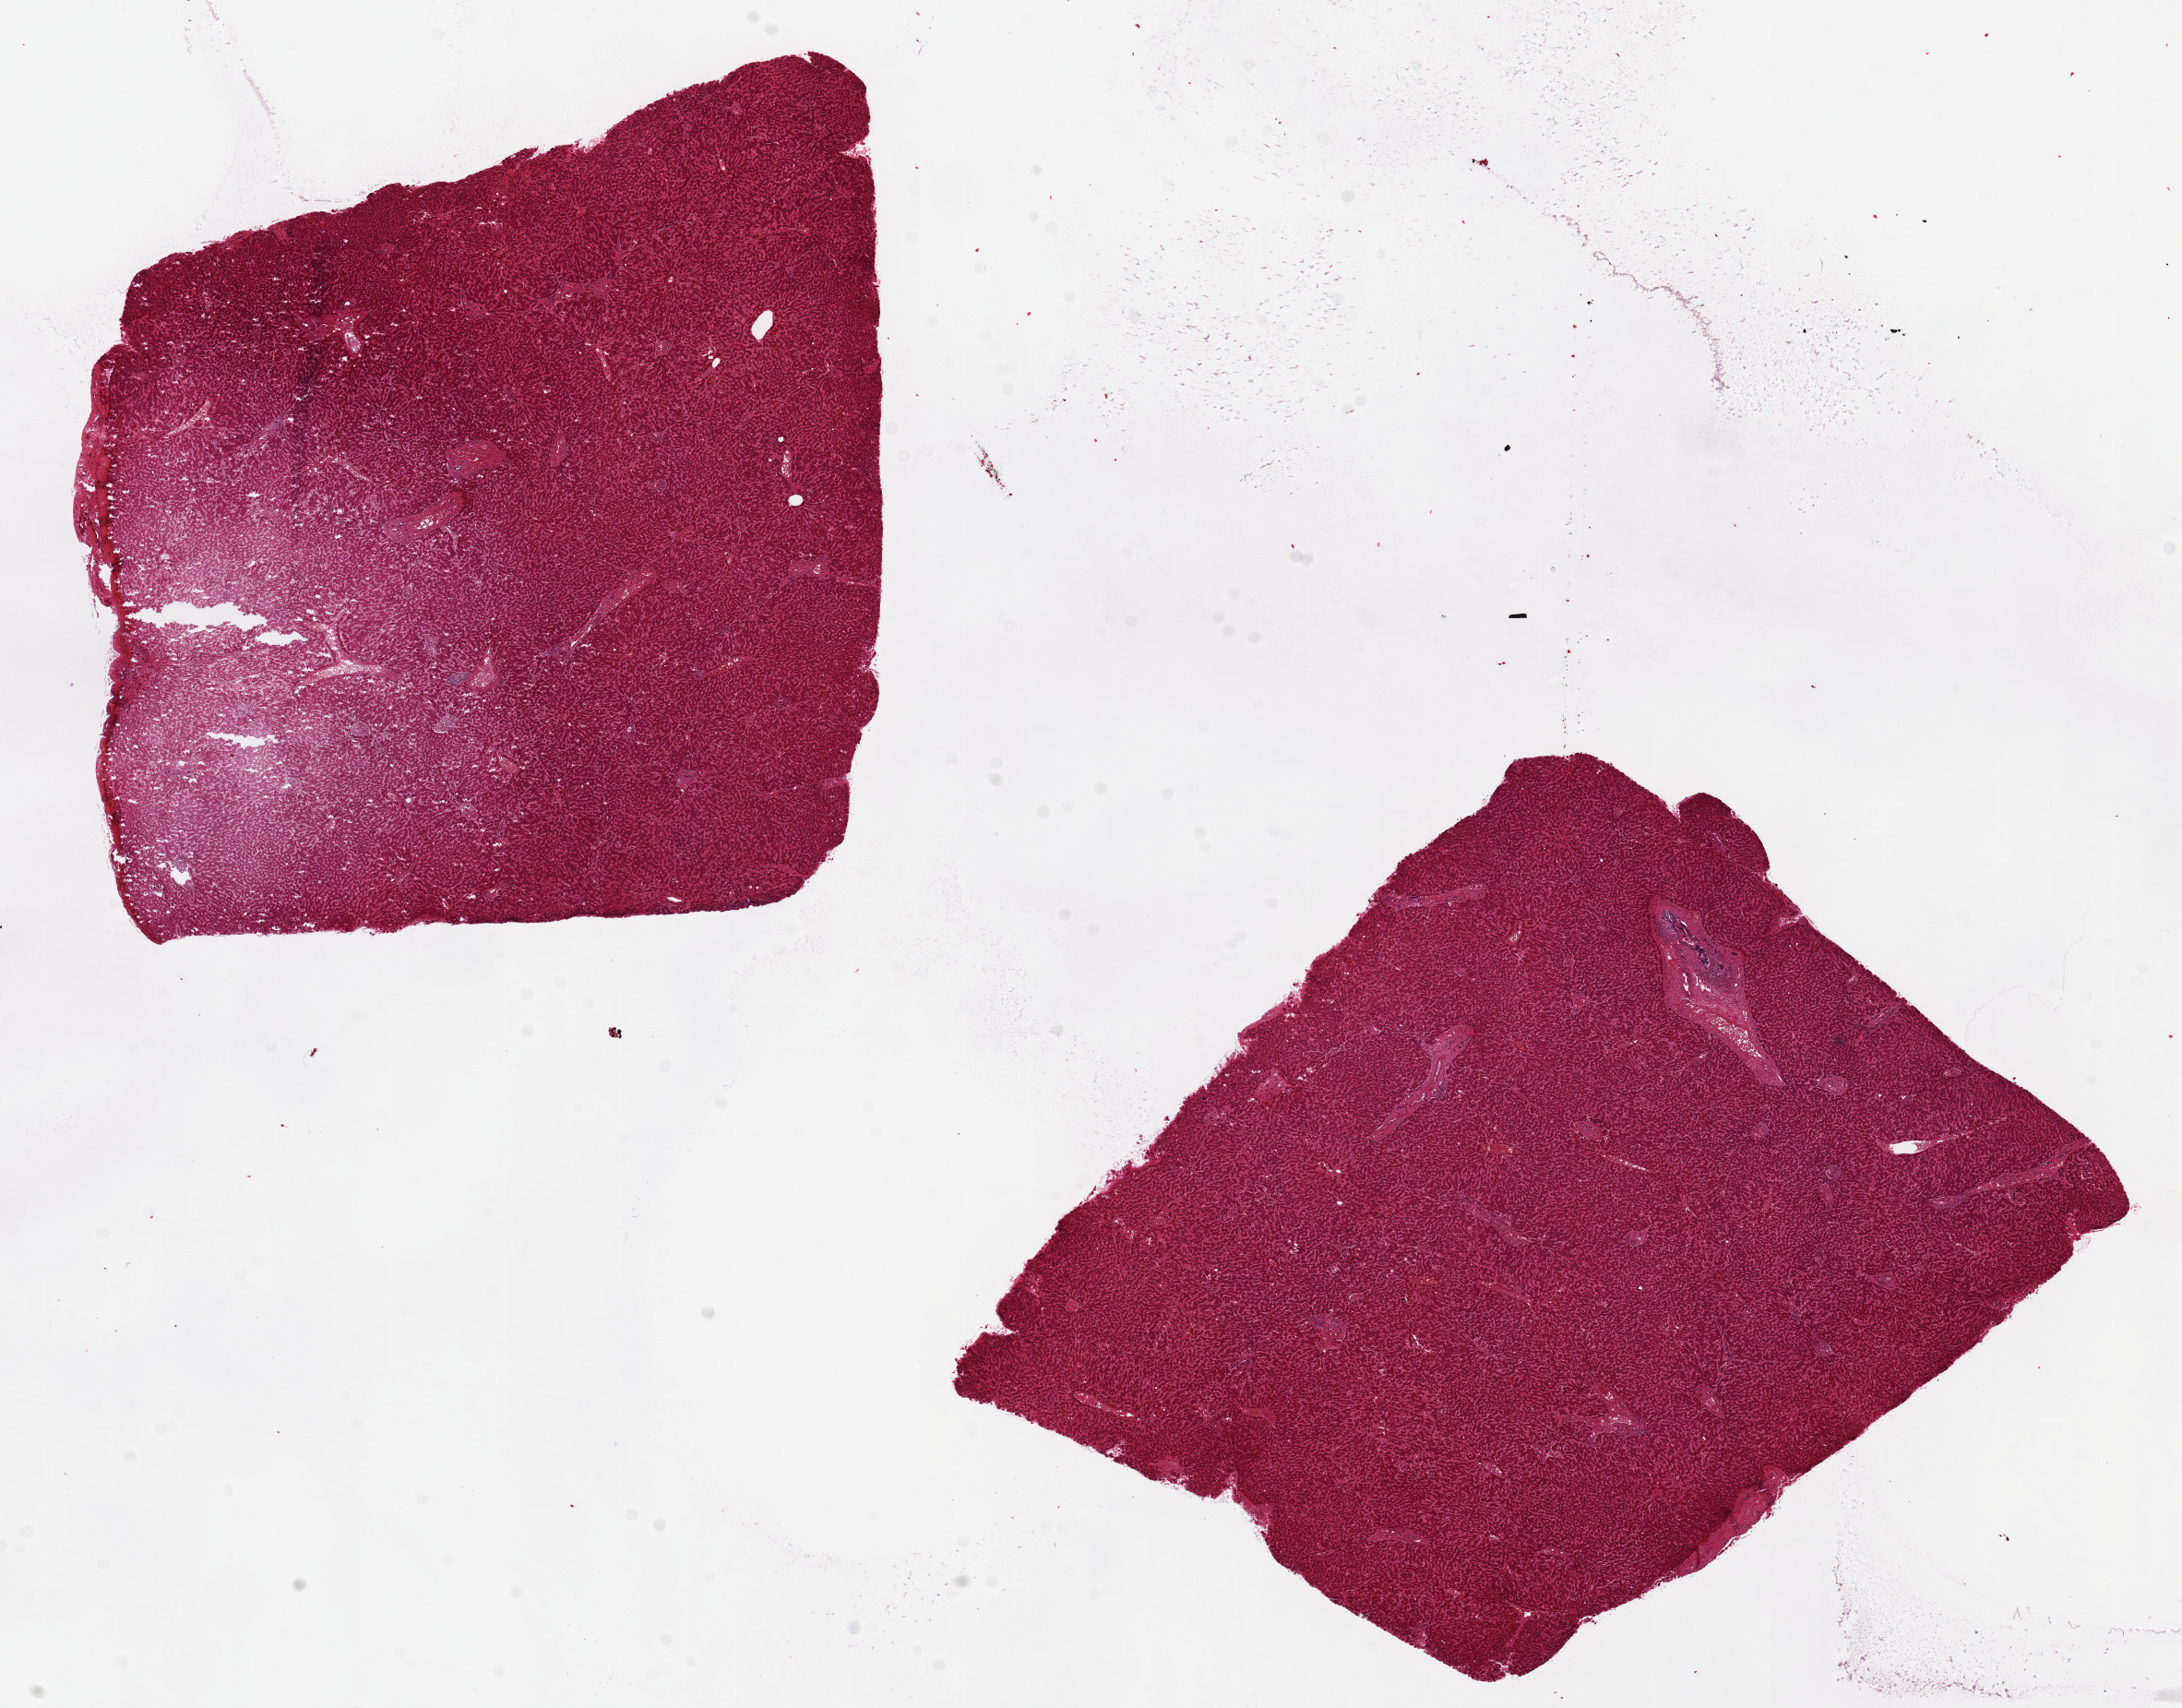
Whole-slide image, haematoxylin and eosin stain — whole scanned area (about 18.7 x 14.6 mm, acquisition: 20x scan) shown as a low-resolution overview. PAXgene-fixed, paraffin-embedded tissue. Target tissue: liver. Tissue donor sample. Donor: male.
Pathologist's review note for this sample: pieces.